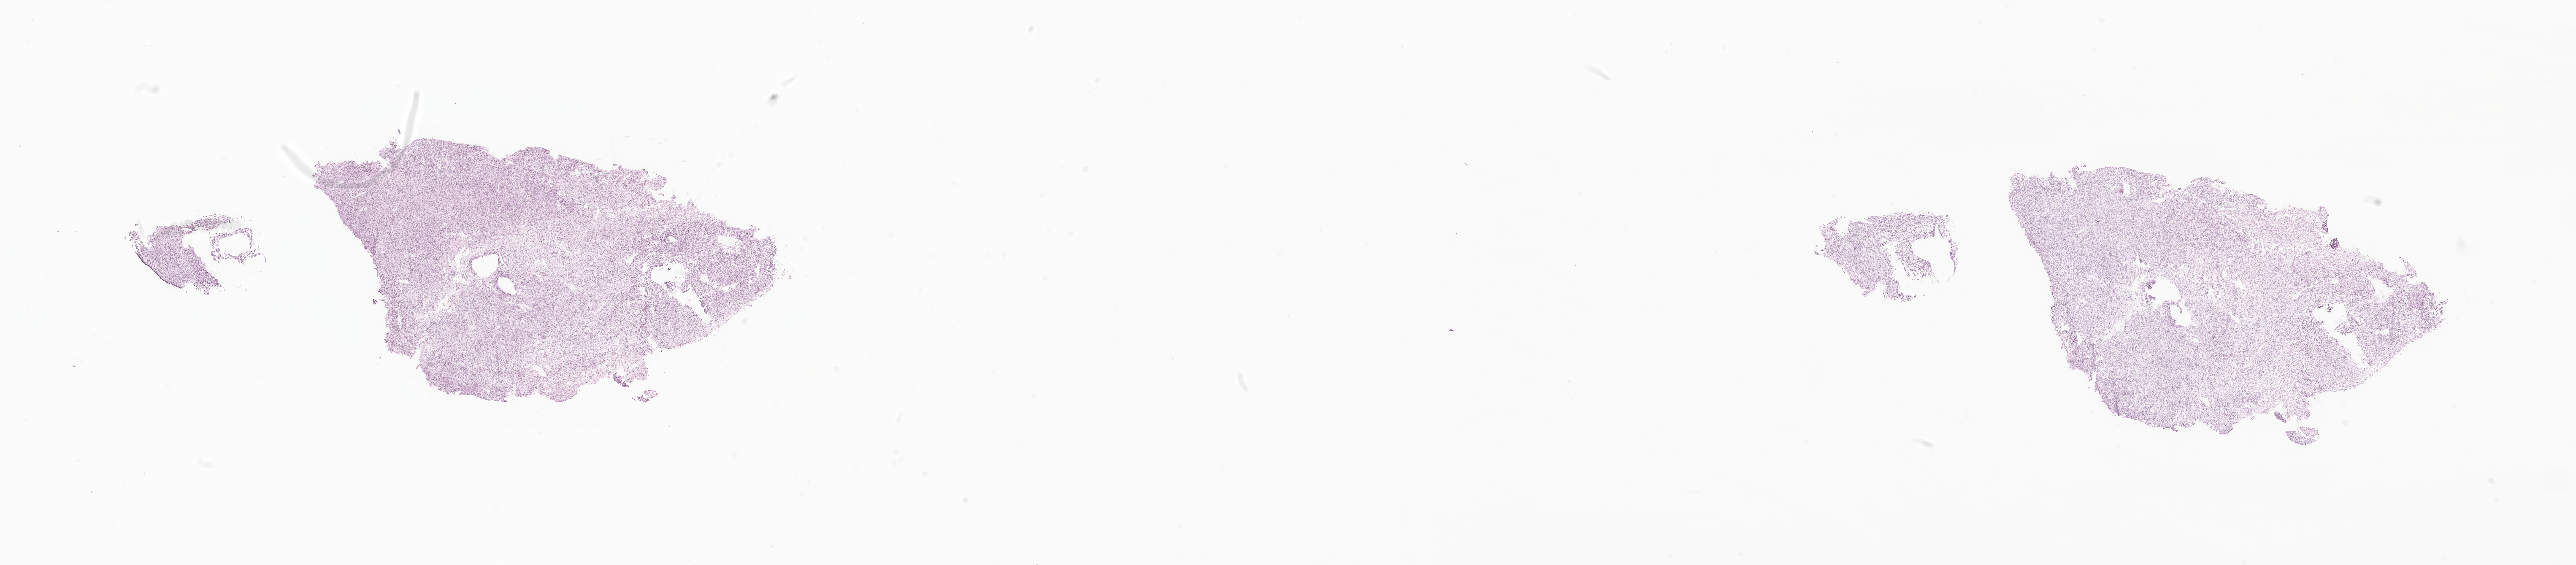
Digitized haematoxylin and eosin-stained section of tumor tissue from the abdomen, whole scanned area (about 39.4 x 8.6 mm) shown as a low-resolution overview, cryosection (OCT / tissue freezing medium). Patient male; age 327 days.
• diagnosis (ICD-O-3 morphology term): Myofibroma